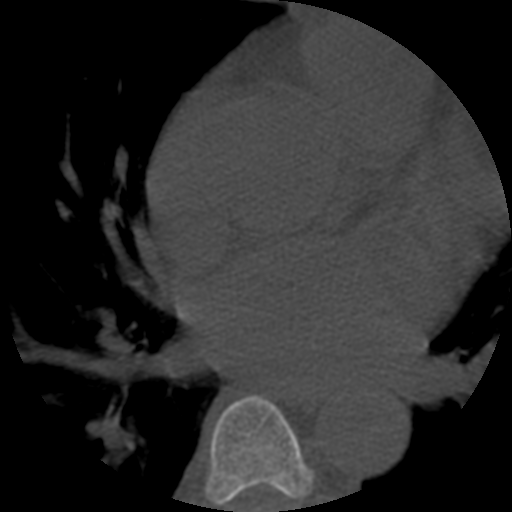
CT including the spine, one axial slice; slice 351 of 508 in the series (ordered by position); 120 kVp; bone window (W 1800 / L 400 HU); 1.25 mm slice thickness; 512 × 512 image matrix. Patient age 57 years. Case-level facts recorded for this patient, not image findings: primary cancer: prostate.
Outlined on this slice (semi-automatic segmentation, software-assisted and operator-edited):
- T6 vertebra: bounding box (x1, y1, x2, y2) in pixels: (205, 396, 314, 507)